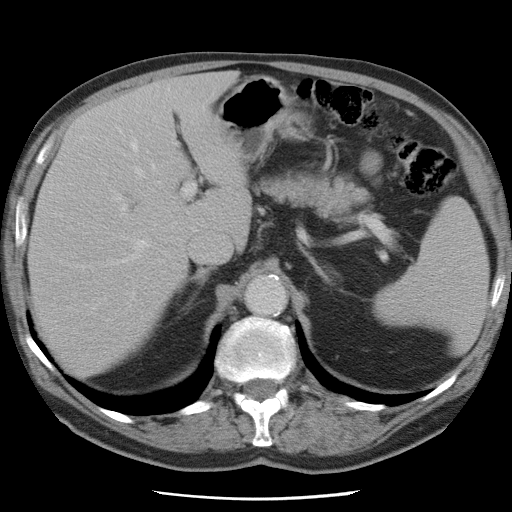
Contrast-enhanced abdominal CT, one axial slice. Position 50 of 78 along the scan axis. Intravenous contrast given. Soft-tissue window (W 400 / L 40 HU). 512 × 512 image matrix, field of view 337 × 337 mm. Male patient, age 75 years. Case-level facts recorded for this patient, not image findings: diagnosis: colorectal cancer liver metastases, imaged before liver resection; multiple liver metastases: yes; largest metastasis: 2.4 cm; disease in both lobes: yes.
Structures marked on this image (expert manual segmentation):
- hepatic veins: bounding box <54,141,160,269> (left, top, right, bottom; pixels)
- liver: <29,74,251,378>
- planned liver remnant (the part of the liver to remain after resection): <29,124,194,378>
- portal vein (with intrahepatic branches): <110,143,196,213>